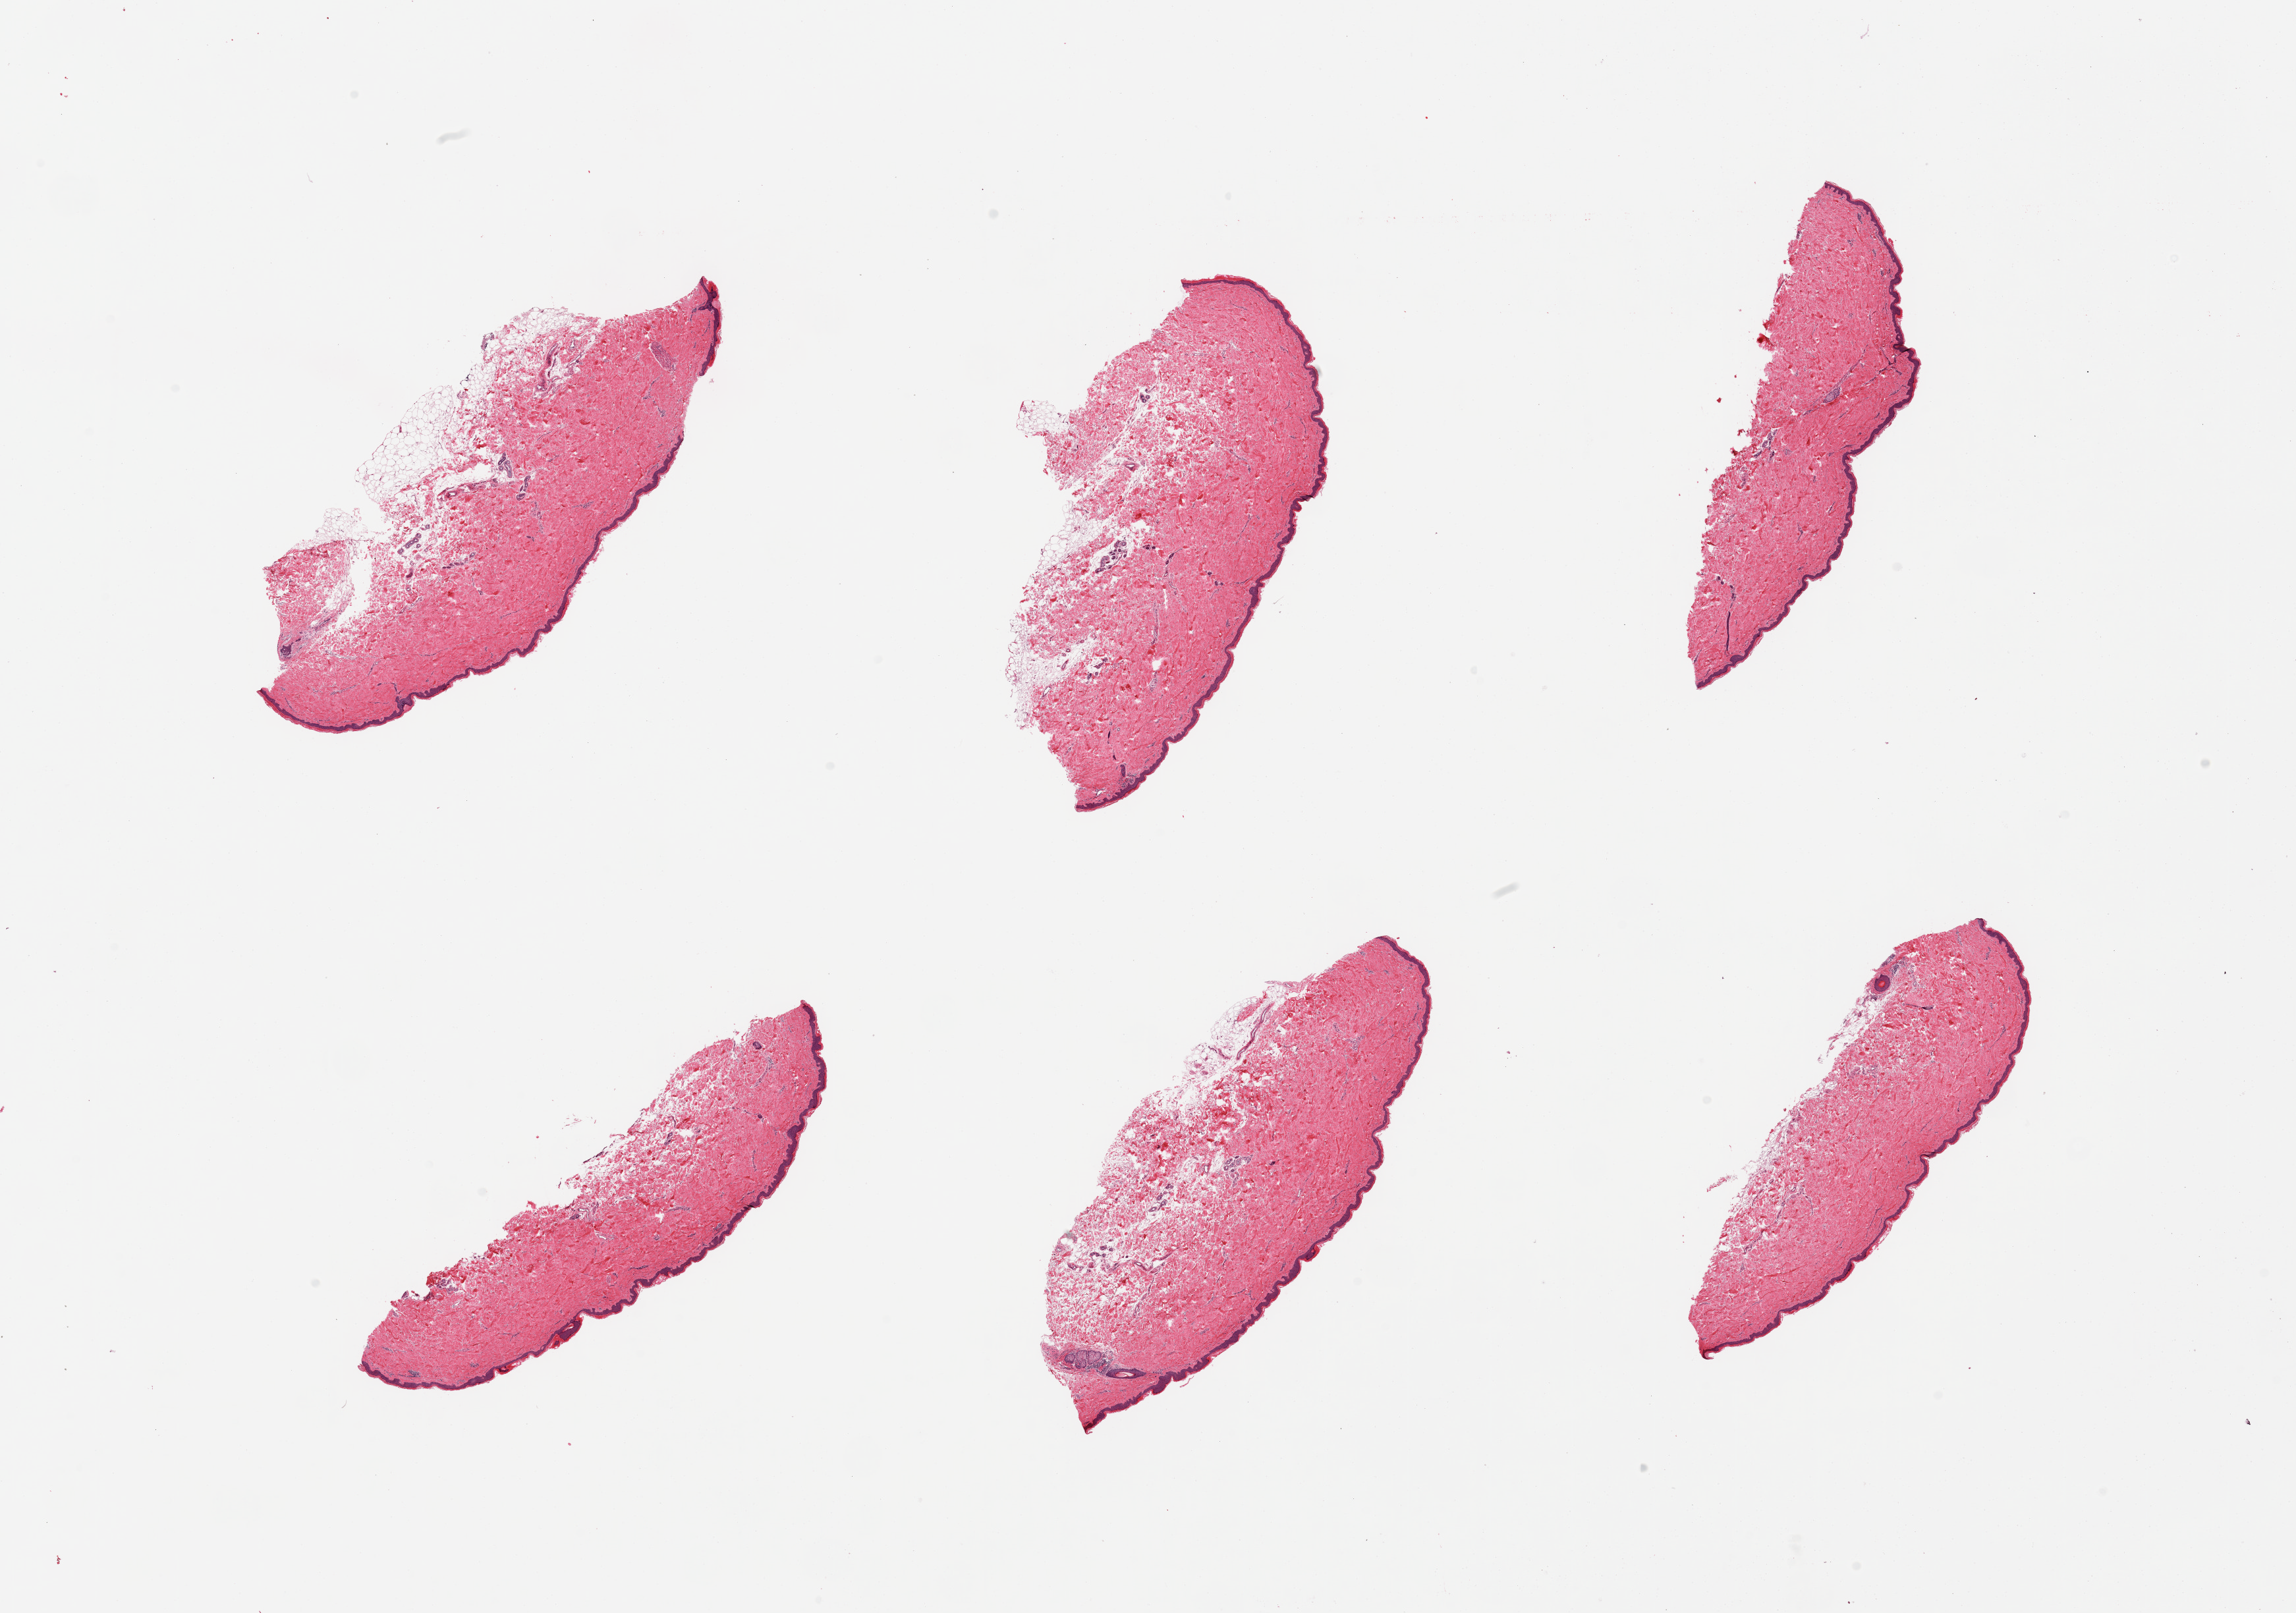
Whole-slide image, haematoxylin and eosin stain, a low-resolution overview of the entire scanned area, about 27.6 x 19.4 mm (from a 20x scan); PAXgene-fixed paraffin-embedded (PFPE) section; section of skin of suprapubic region (target tissue); tissue donor sample. Donor: female.
Pathologist's review note for this sample: 6 pieces, squamous epithelium is ~60microns thick. Minimal adherent dermal fat.